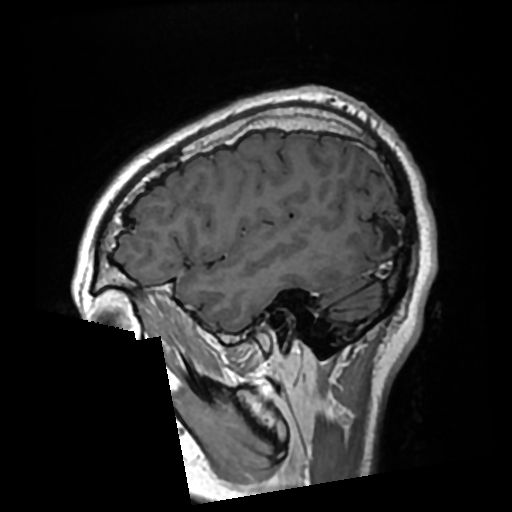
Brain MRI from a brain-tumour surgery series, one sagittal slice. Slice 74 of 276 in the series (ordered by position). T1-weighted post-contrast. 0.7 mm slice thickness. 512 × 512 image matrix, field of view 250 × 250 mm. Case-level facts recorded for this patient, not image findings: histopathology: Glioma with ependymal features; WHO grade: 2; tumour location: Left Parietal.
Annotated regions visible in this slice (outlined manually by an expert reader):
- previous resection cavity: box from (x=373, y=225) to (x=393, y=247) px